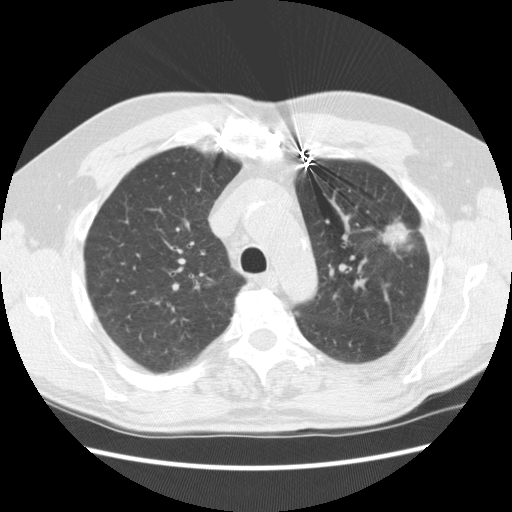
Low-dose screening chest CT, axial slice; baseline annual screen; lung window (W 1500 / L -600 HU); 2.5 mm slice thickness; standard (soft-tissue) reconstruction kernel (STANDARD); slice 177 of 231 in the series. Male, age 72 years at enrolment.
Lesion marked by an expert reader, bounding box [x1, y1, x2, y2] px = [347, 197, 428, 260]. Reader record for this screening exam (exam-level; its link to the box is not recorded): non-calcified nodule or mass ≥4 mm, left upper lobe, 25 × 18 mm, spiculated (stellate) margins, soft tissue attenuation. Official screen result: positive, change unspecified: nodule(s) >= 4 mm or enlarging nodule(s), mass(es), or other non-specific abnormalities suspicious for lung cancer. Later outcome: lung cancer diagnosed 35 days after this screen — adenocarcinoma, NOS, left upper lobe, well differentiated (G1), stage IIIB (AJCC 6th edition), 25 mm at pathology.